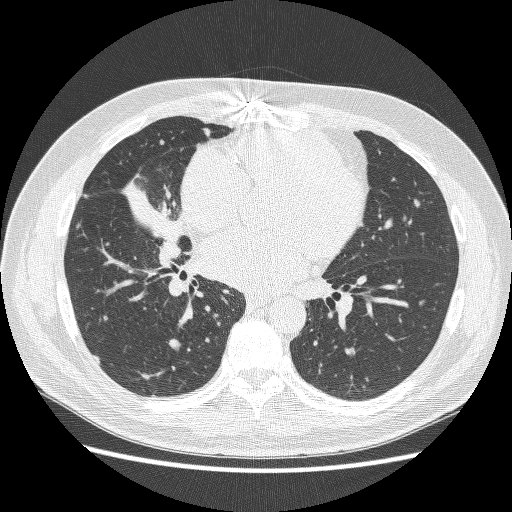
Low-dose screening chest CT, axial slice, baseline annual screen, lung window (W 1500 / L -600 HU), 512 × 512 image matrix, field of view 360 × 360 mm. Male, age 59 years at enrolment. Former smoker at enrolment.
- Expert reader's lesion annotation, bounding box [x1, y1, x2, y2] px = [113, 166, 196, 250].
- No non-calcified nodule or mass ≥4 mm was recorded by the screening reader at this exam.
- Lung cancer was diagnosed 24 days after this screen: adenocarcinoma, NOS, right middle lobe, poorly differentiated (G3), stage IV (AJCC 6th edition), 54 mm at pathology.